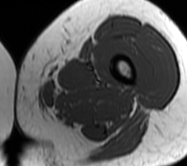
MRI of an extremity soft-tissue mass, one axial slice. MR volume resampled by the dataset authors to the PET/CT grid (not the native acquisition matrix). 187 × 166 image matrix, field of view 183 × 162 mm. Female patient. From the clinical record (not read from this slice): histological type: leiomyosarcoma; grade: high; site of the primary tumour: groin.
Annotated regions visible in this slice (expert contour drawn on MRI and transferred to this co-registered scan by the dataset authors):
- gross tumour volume including surrounding oedema: bounding box (x1, y1, x2, y2) in pixels: (16, 101, 44, 113)